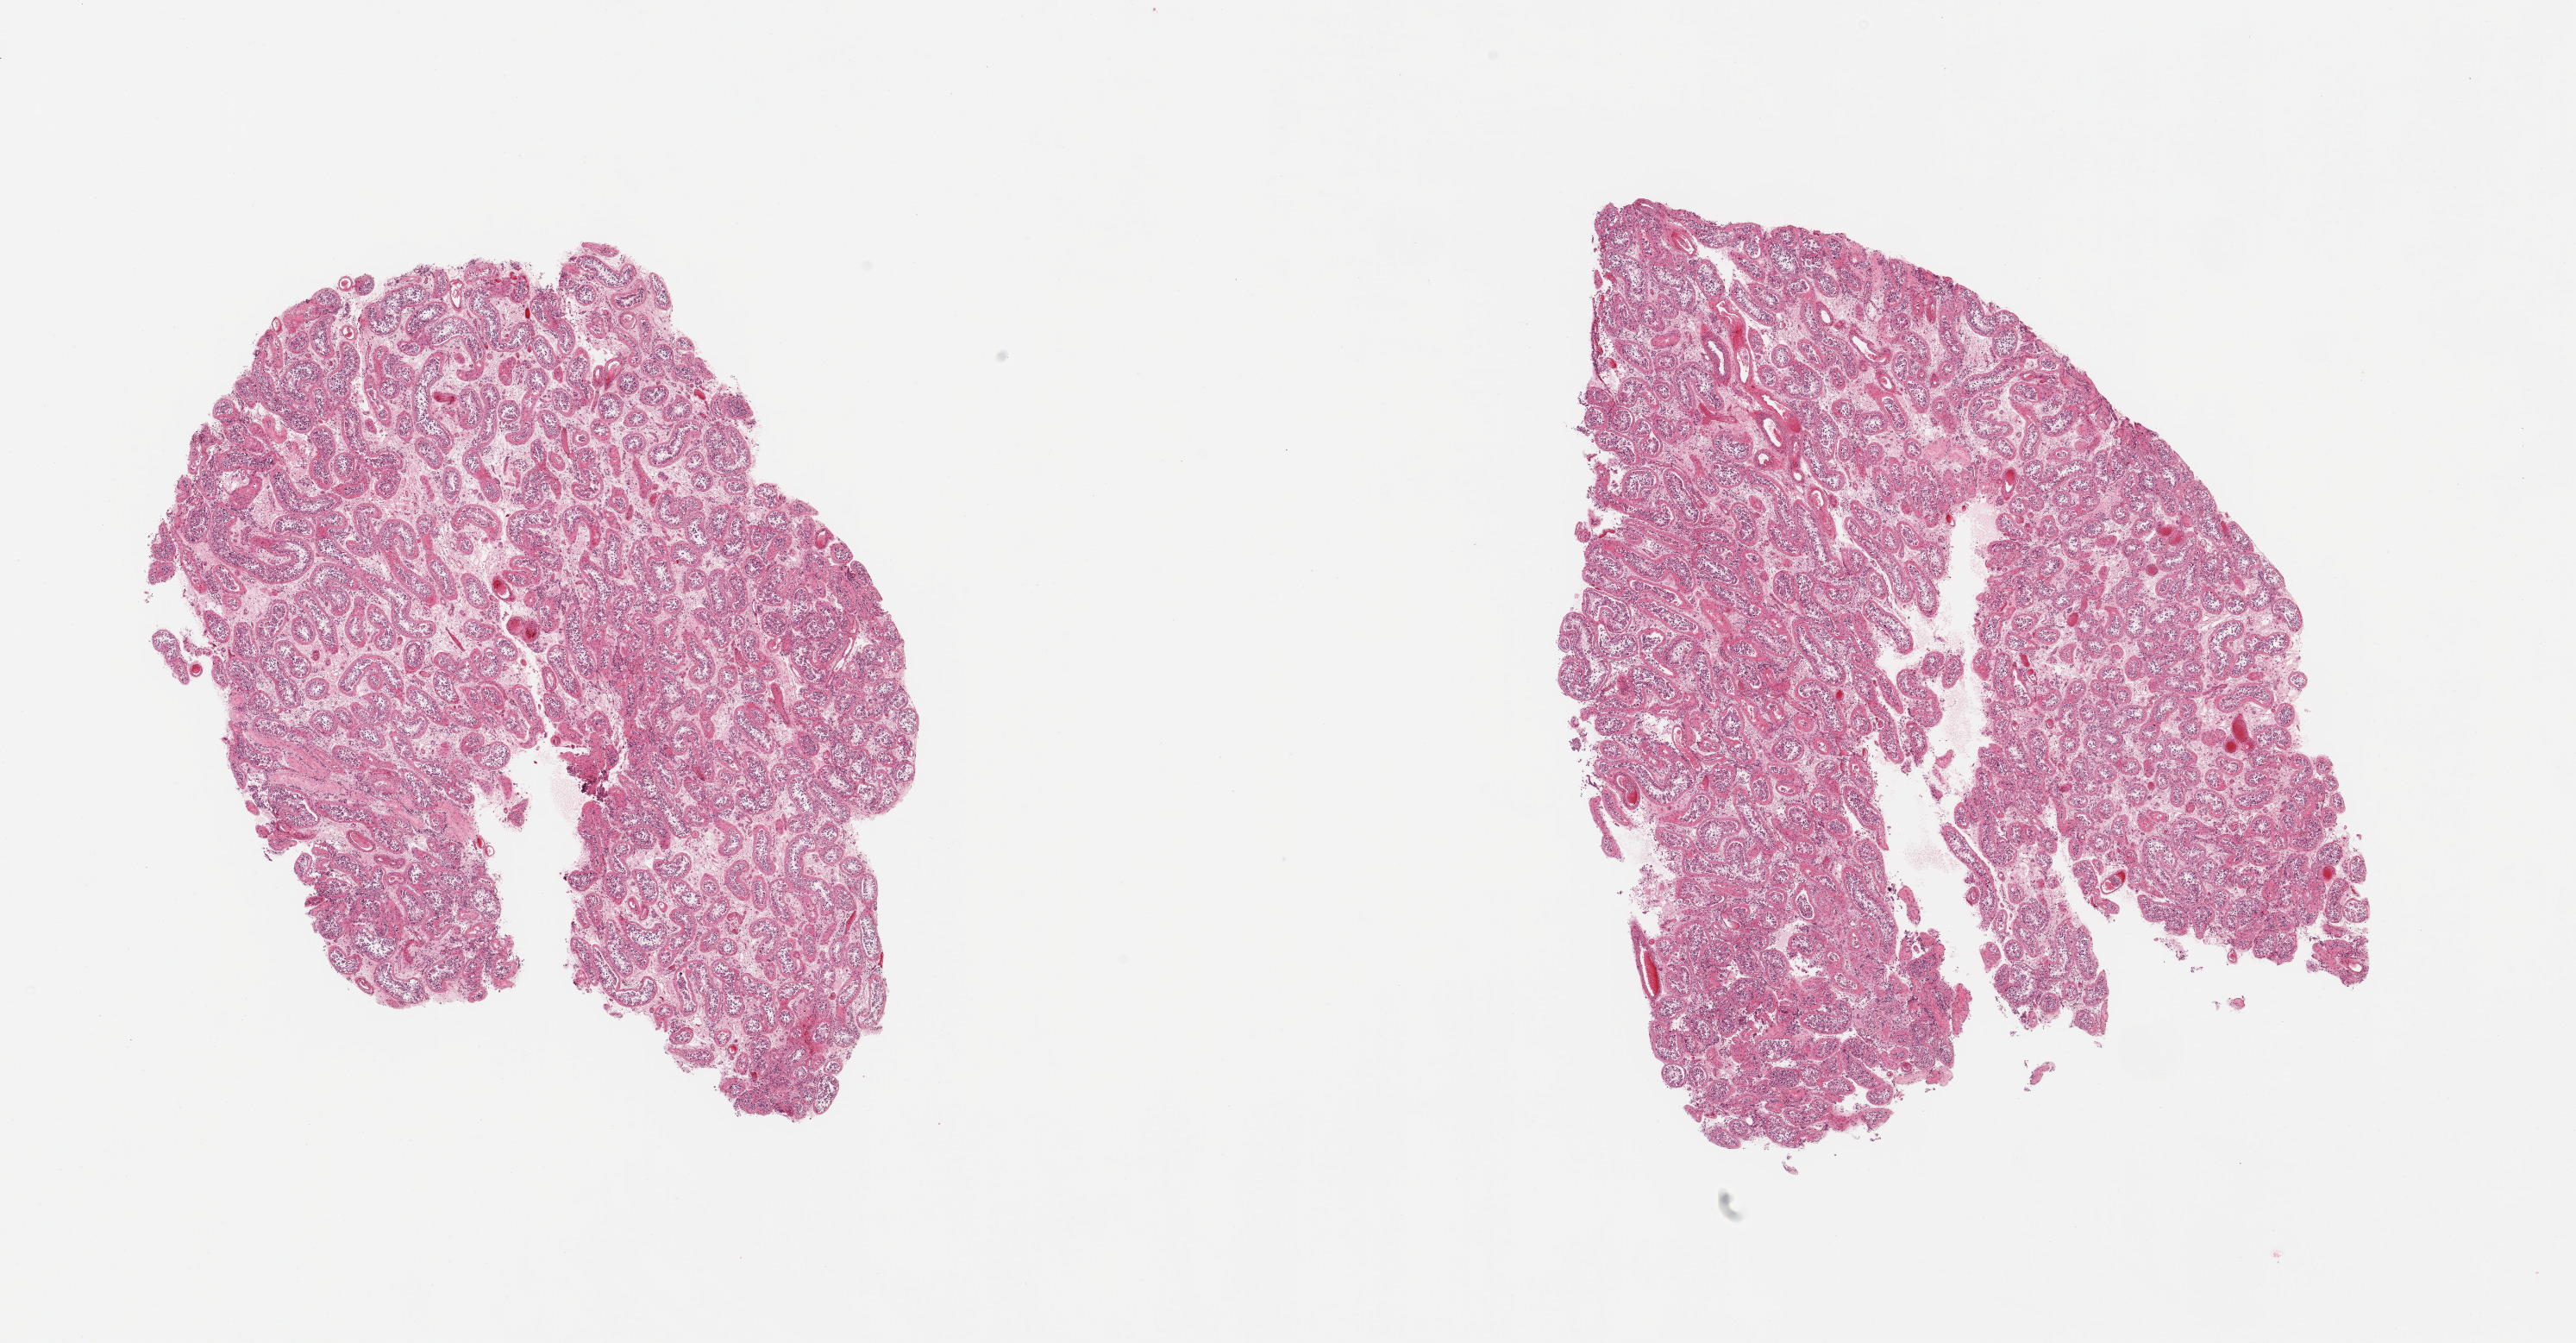
Hematoxylin and eosin (H&E) whole-slide image, brightfield, shown as a low-resolution overview of the whole scanned area (about 23.6 x 12.3 mm). PAXgene-fixed paraffin-embedded (PFPE) section. Sampled site (target tissue): testis. Donor tissue sample. Male donor.
* reviewer comment on this tissue sample: 2 pieces, spermatogenesis